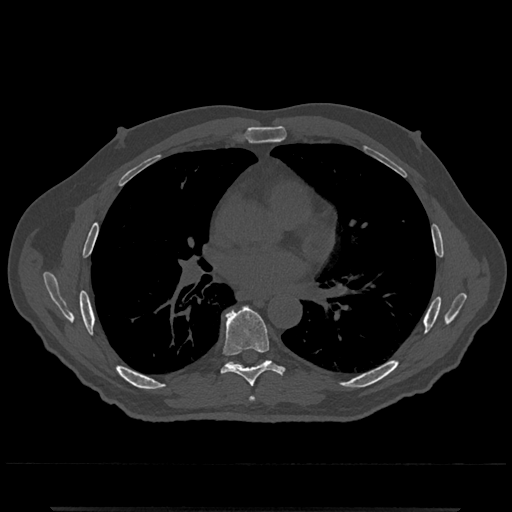
CT including the spine, one axial slice. Position 717 of 797 along the scan axis. 120 kVp. Bone window (W 1800 / L 400 HU). 0.5 mm slice thickness. 512 × 512 image matrix, field of view 393 × 393 mm. Patient: male, 67 years. From the clinical record (not read from this slice): primary cancer: prostate.
Outlined on this slice (semi-automatically segmented with operator editing):
- T6 vertebra: bounding box (x1, y1, x2, y2) in pixels: (235, 363, 255, 402)
- T7 vertebra: (221, 307, 282, 387)
- T8 vertebra: (227, 362, 264, 365)